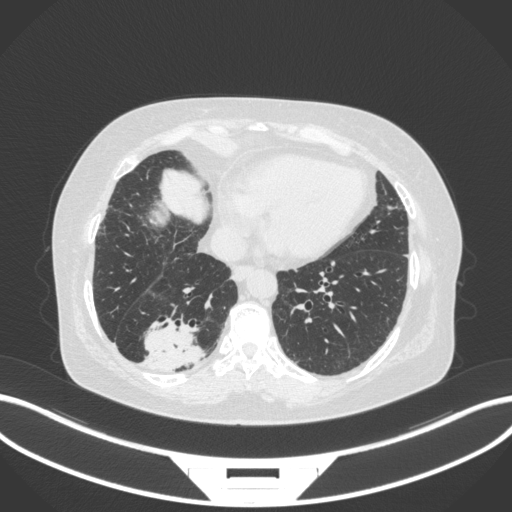
Chest CT, one axial slice. Position 67 of 303 along the scan axis. Reconstruction kernel B31f. Lung window (W 1500 / L -600 HU). 512 × 512 image matrix, field of view 400 × 400 mm. Patient: female, 65 years. Case-level facts recorded for this patient, not image findings: clinical TNM (as recorded): T2b N1 M0.
Structures marked on this image (rectangle marked by the reading radiologist):
- lung tumour (recorded histology: adenocarcinoma): bounding box <136,316,208,377> (left, top, right, bottom; pixels)